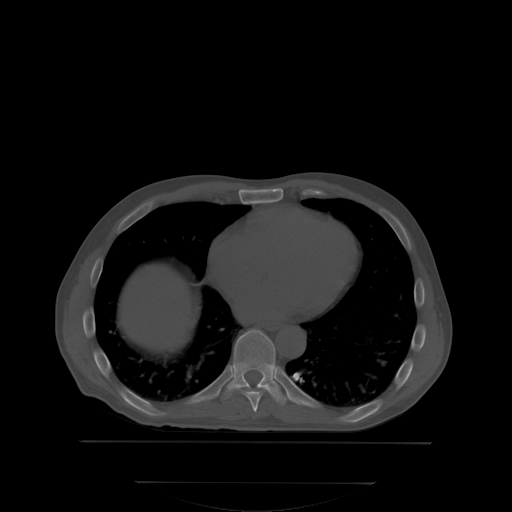
CT including the spine, one axial slice; slice 209 of 350 in the series (ordered by position); bone window (W 1800 / L 400 HU); 512 × 512 image matrix, field of view 500 × 500 mm. Patient: male, 58 years. From the clinical record (not read from this slice): primary cancer: prostate.
Structures marked on this image (semi-automatic segmentation, software-assisted and operator-edited):
- T8 vertebra: bounding box (x1, y1, x2, y2) in pixels: (219, 377, 268, 412)
- T9 vertebra: (221, 329, 288, 406)